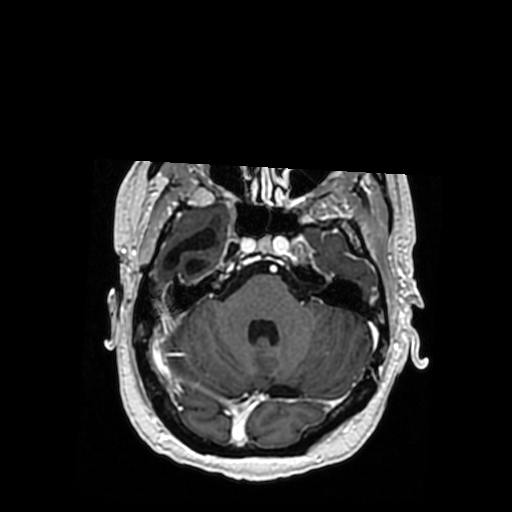
Brain MRI from a brain-tumour surgery series, one axial slice; position 251 of 364 along the scan axis; T1-weighted post-contrast; 0.5 mm slice thickness; 512 × 512 image matrix. Case-level facts recorded for this patient, not image findings: histopathology: Oligodendroglioma; WHO grade: 3; IDH mutation: yes; tumour location: Right Posterior Temporal Inferior Parietal.
Annotated regions visible in this slice (manually delineated by an expert):
- previous resection cavity: bounding box [x1, y1, x2, y2] px = [164, 228, 217, 274]